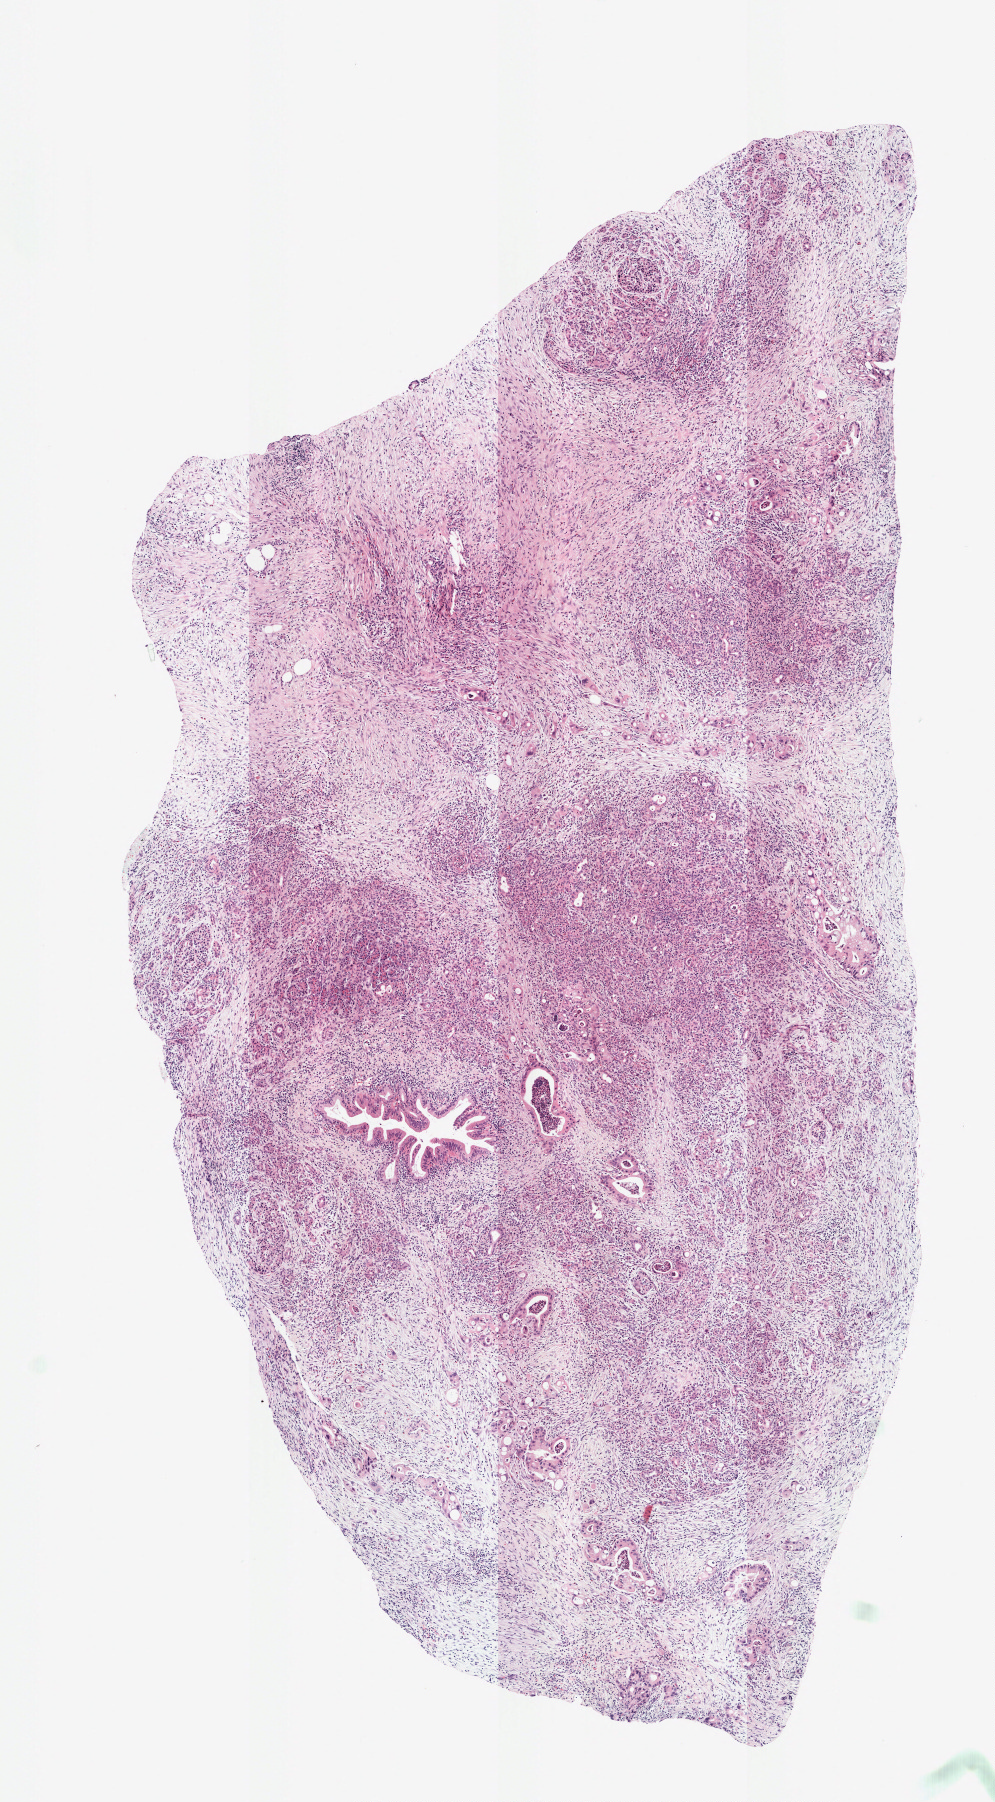
Whole-slide histology image, H&E — a low-resolution overview of the entire scanned area, about 3.9 x 7.1 mm (from a 20x scan); frozen section from the top of the tissue portion; sample: primary tumour, pancreas. Patient: female, age at initial diagnosis 61 years.
Pathologic diagnosis: Infiltrating duct carcinoma, NOS (head of pancreas).